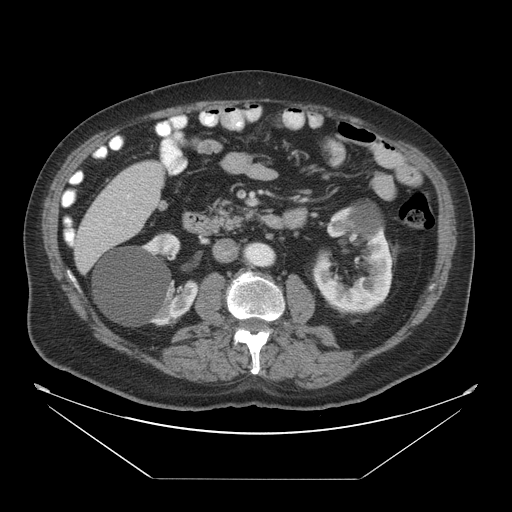
Contrast-enhanced abdominal CT, one axial slice; position 15 of 45 along the scan axis; reconstruction kernel STANDARD; 120 kVp; intravenous contrast given; soft-tissue window (W 400 / L 40 HU); 512 × 512 image matrix, field of view 463 × 463 mm. Male patient, age 87 years. From the clinical record (not read from this slice): diagnosis: colorectal cancer liver metastases, imaged before liver resection; multiple liver metastases: no; largest metastasis: 4.5 cm; disease in both lobes: yes.
Annotated regions visible in this slice (outlined manually by an expert reader):
- liver: bounding box <74,161,166,274> (left, top, right, bottom; pixels)
- portal vein (with intrahepatic branches): <123,213,125,215>